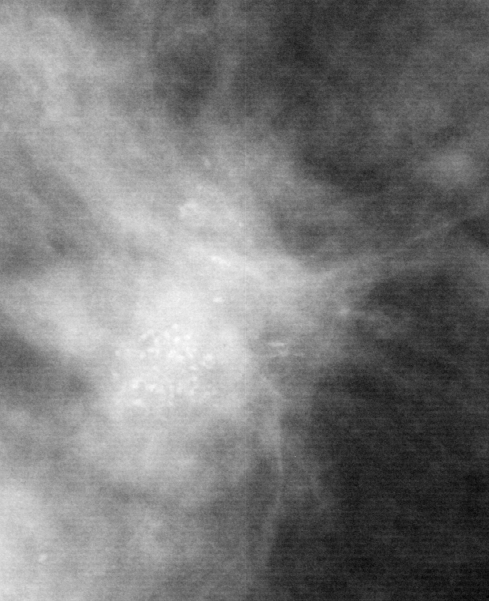
Region of interest cut from a scanned film mammogram (one marked finding); right breast; CC view; BI-RADS breast density category 2 (scale 1–4).
Finding: calcifications, morphology pleomorphic, distribution clustered; BI-RADS assessment category 5; pathology (as recorded): malignant.